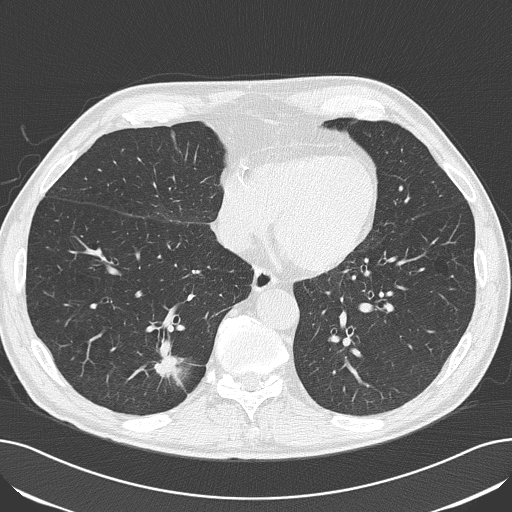
Axial slice from a low-dose chest CT screening exam, first (baseline) screen, lung window (W 1500 / L -600 HU), 2 mm slice thickness, lung (sharp) reconstruction kernel (B50f), slice 123 of 182 in the series. Male, age 71 years at enrolment.
Expert reader's lesion annotation, bounding box <134,331,195,394> (left, top, right, bottom; pixels). The exam's reader record, not a measurement of the box and not confirmed to be the same lesion: non-calcified nodule or mass ≥4 mm, right lower lobe, 14 × 14 mm, spiculated (stellate) margins, soft tissue attenuation.